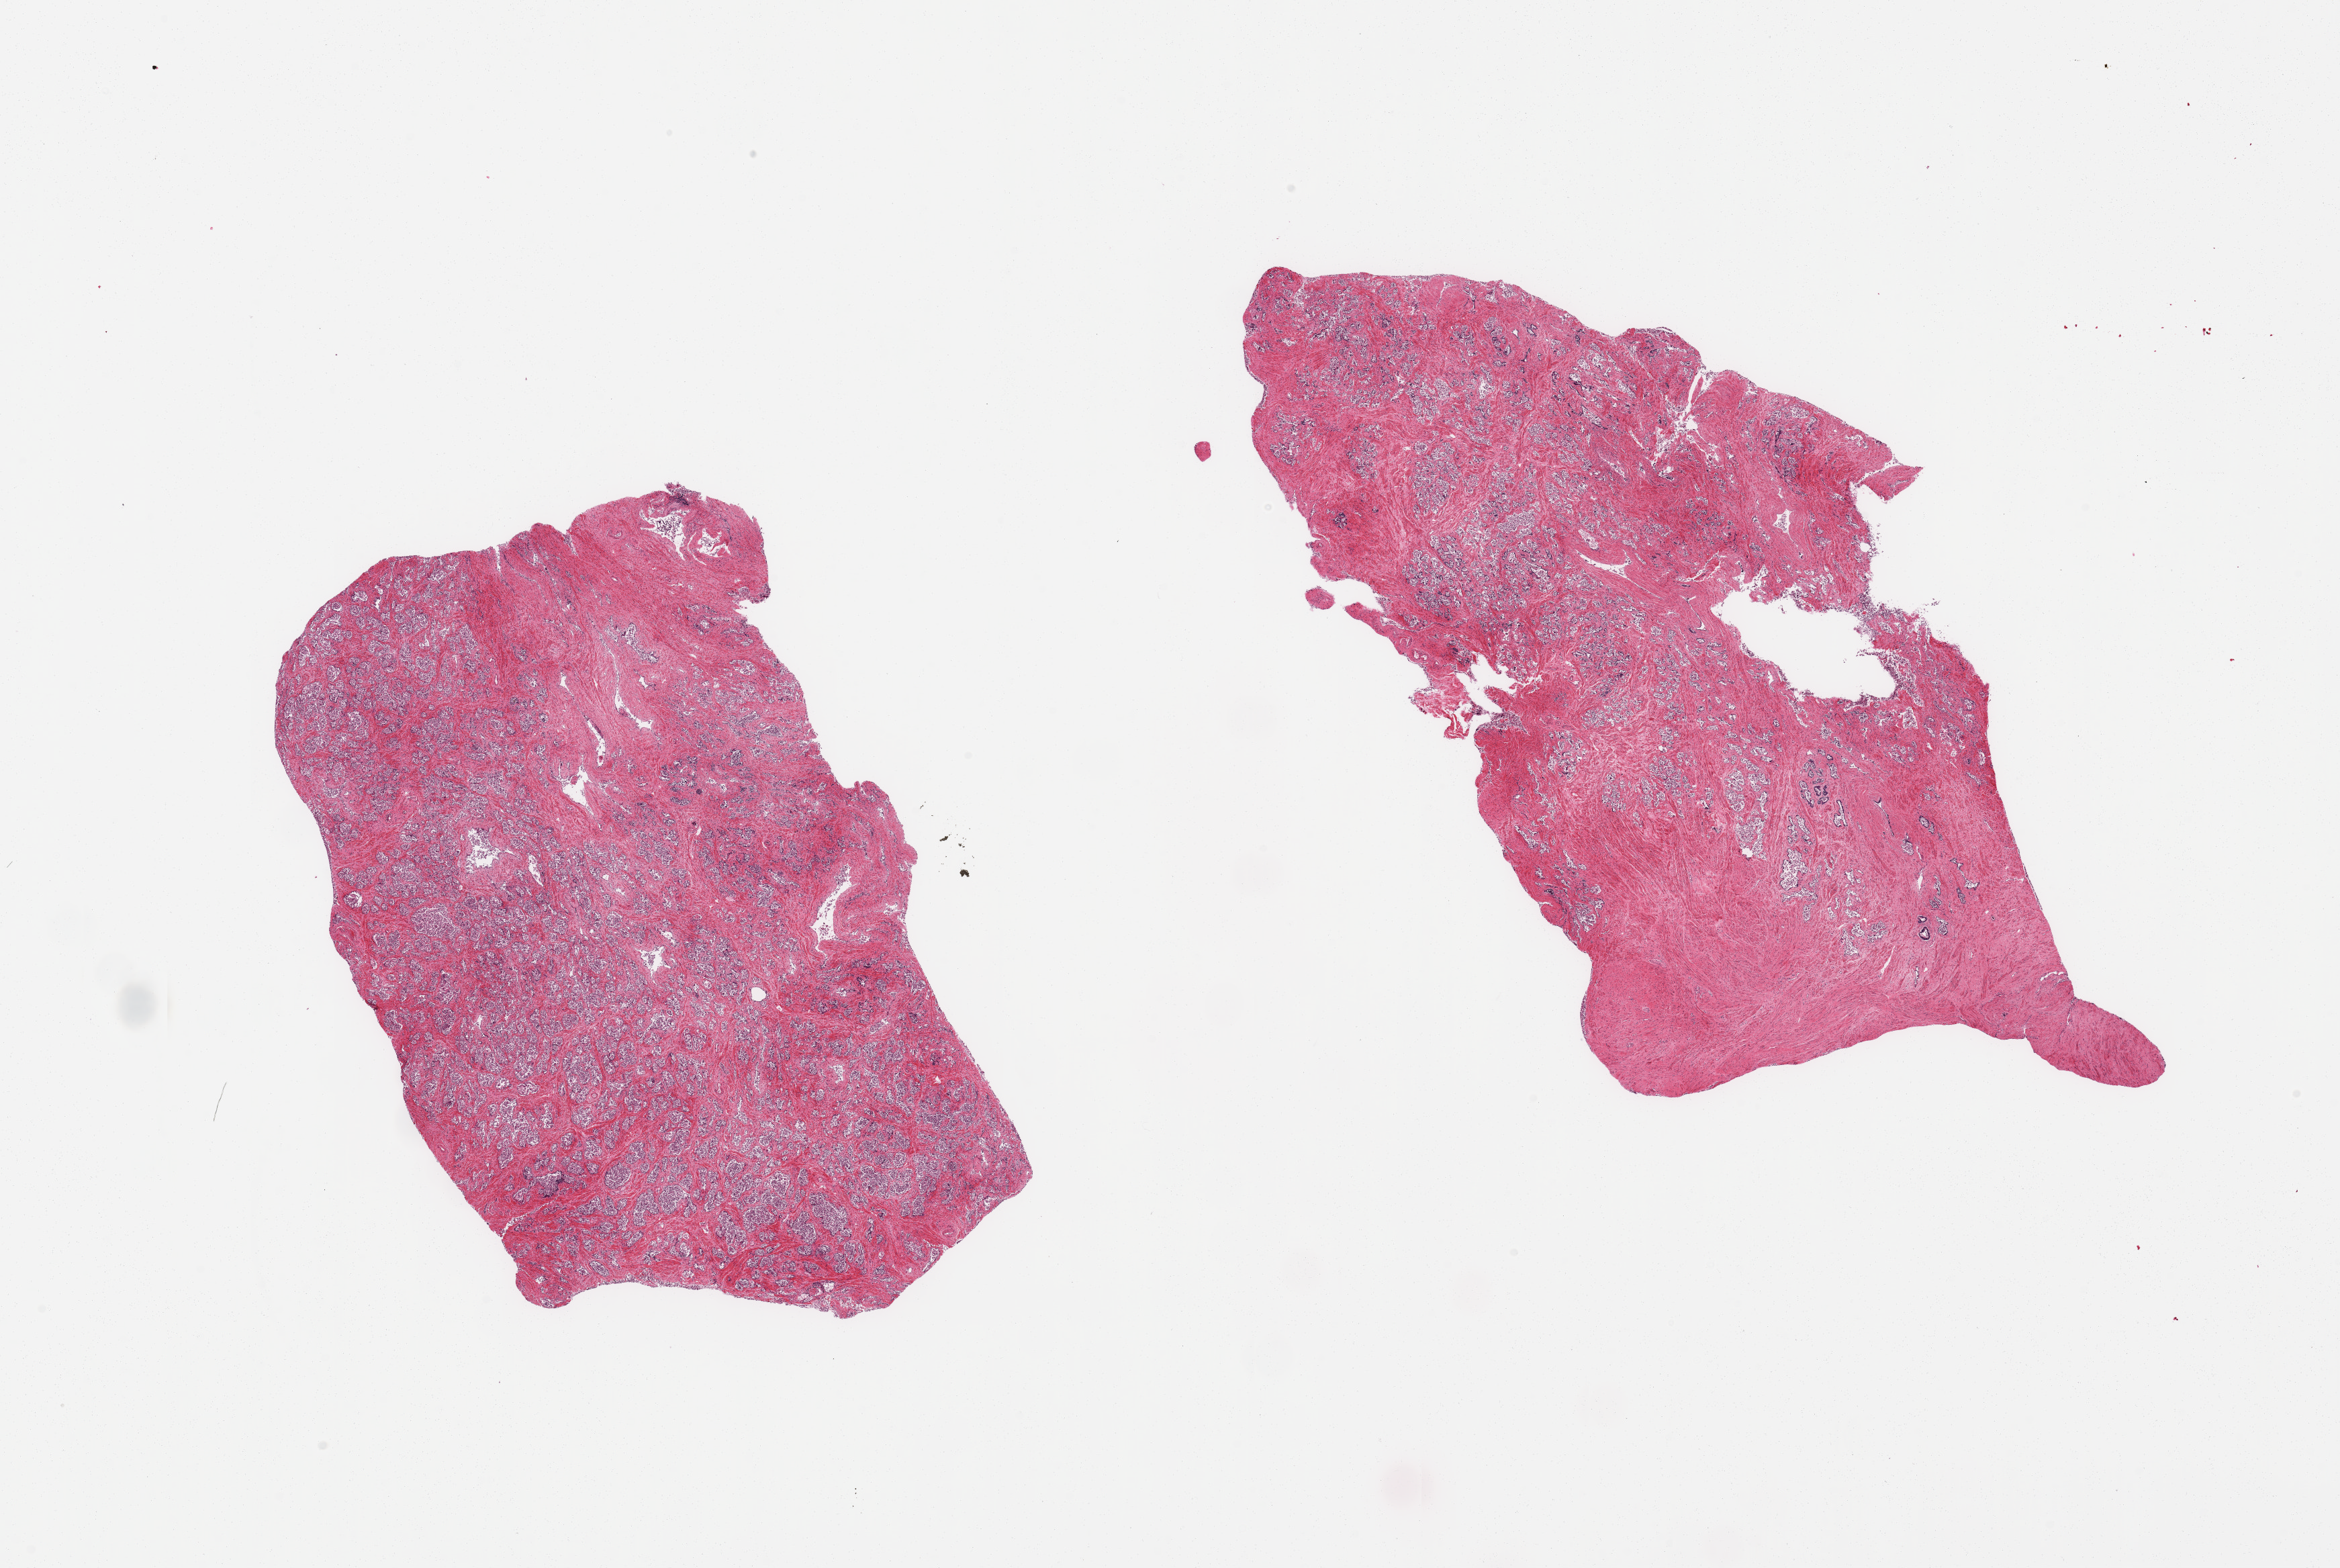
H&E whole-slide image, brightfield — a low-resolution overview of the entire scanned area, about 27.6 x 18.5 mm (slide scanned at 20x). PAXgene-fixed, paraffin-embedded tissue. Sampled site (target tissue): prostate. Donor tissue sample. Donor sex: male.
Reviewer comment on this tissue sample: 2 pieces, advanced glandular autolysis.